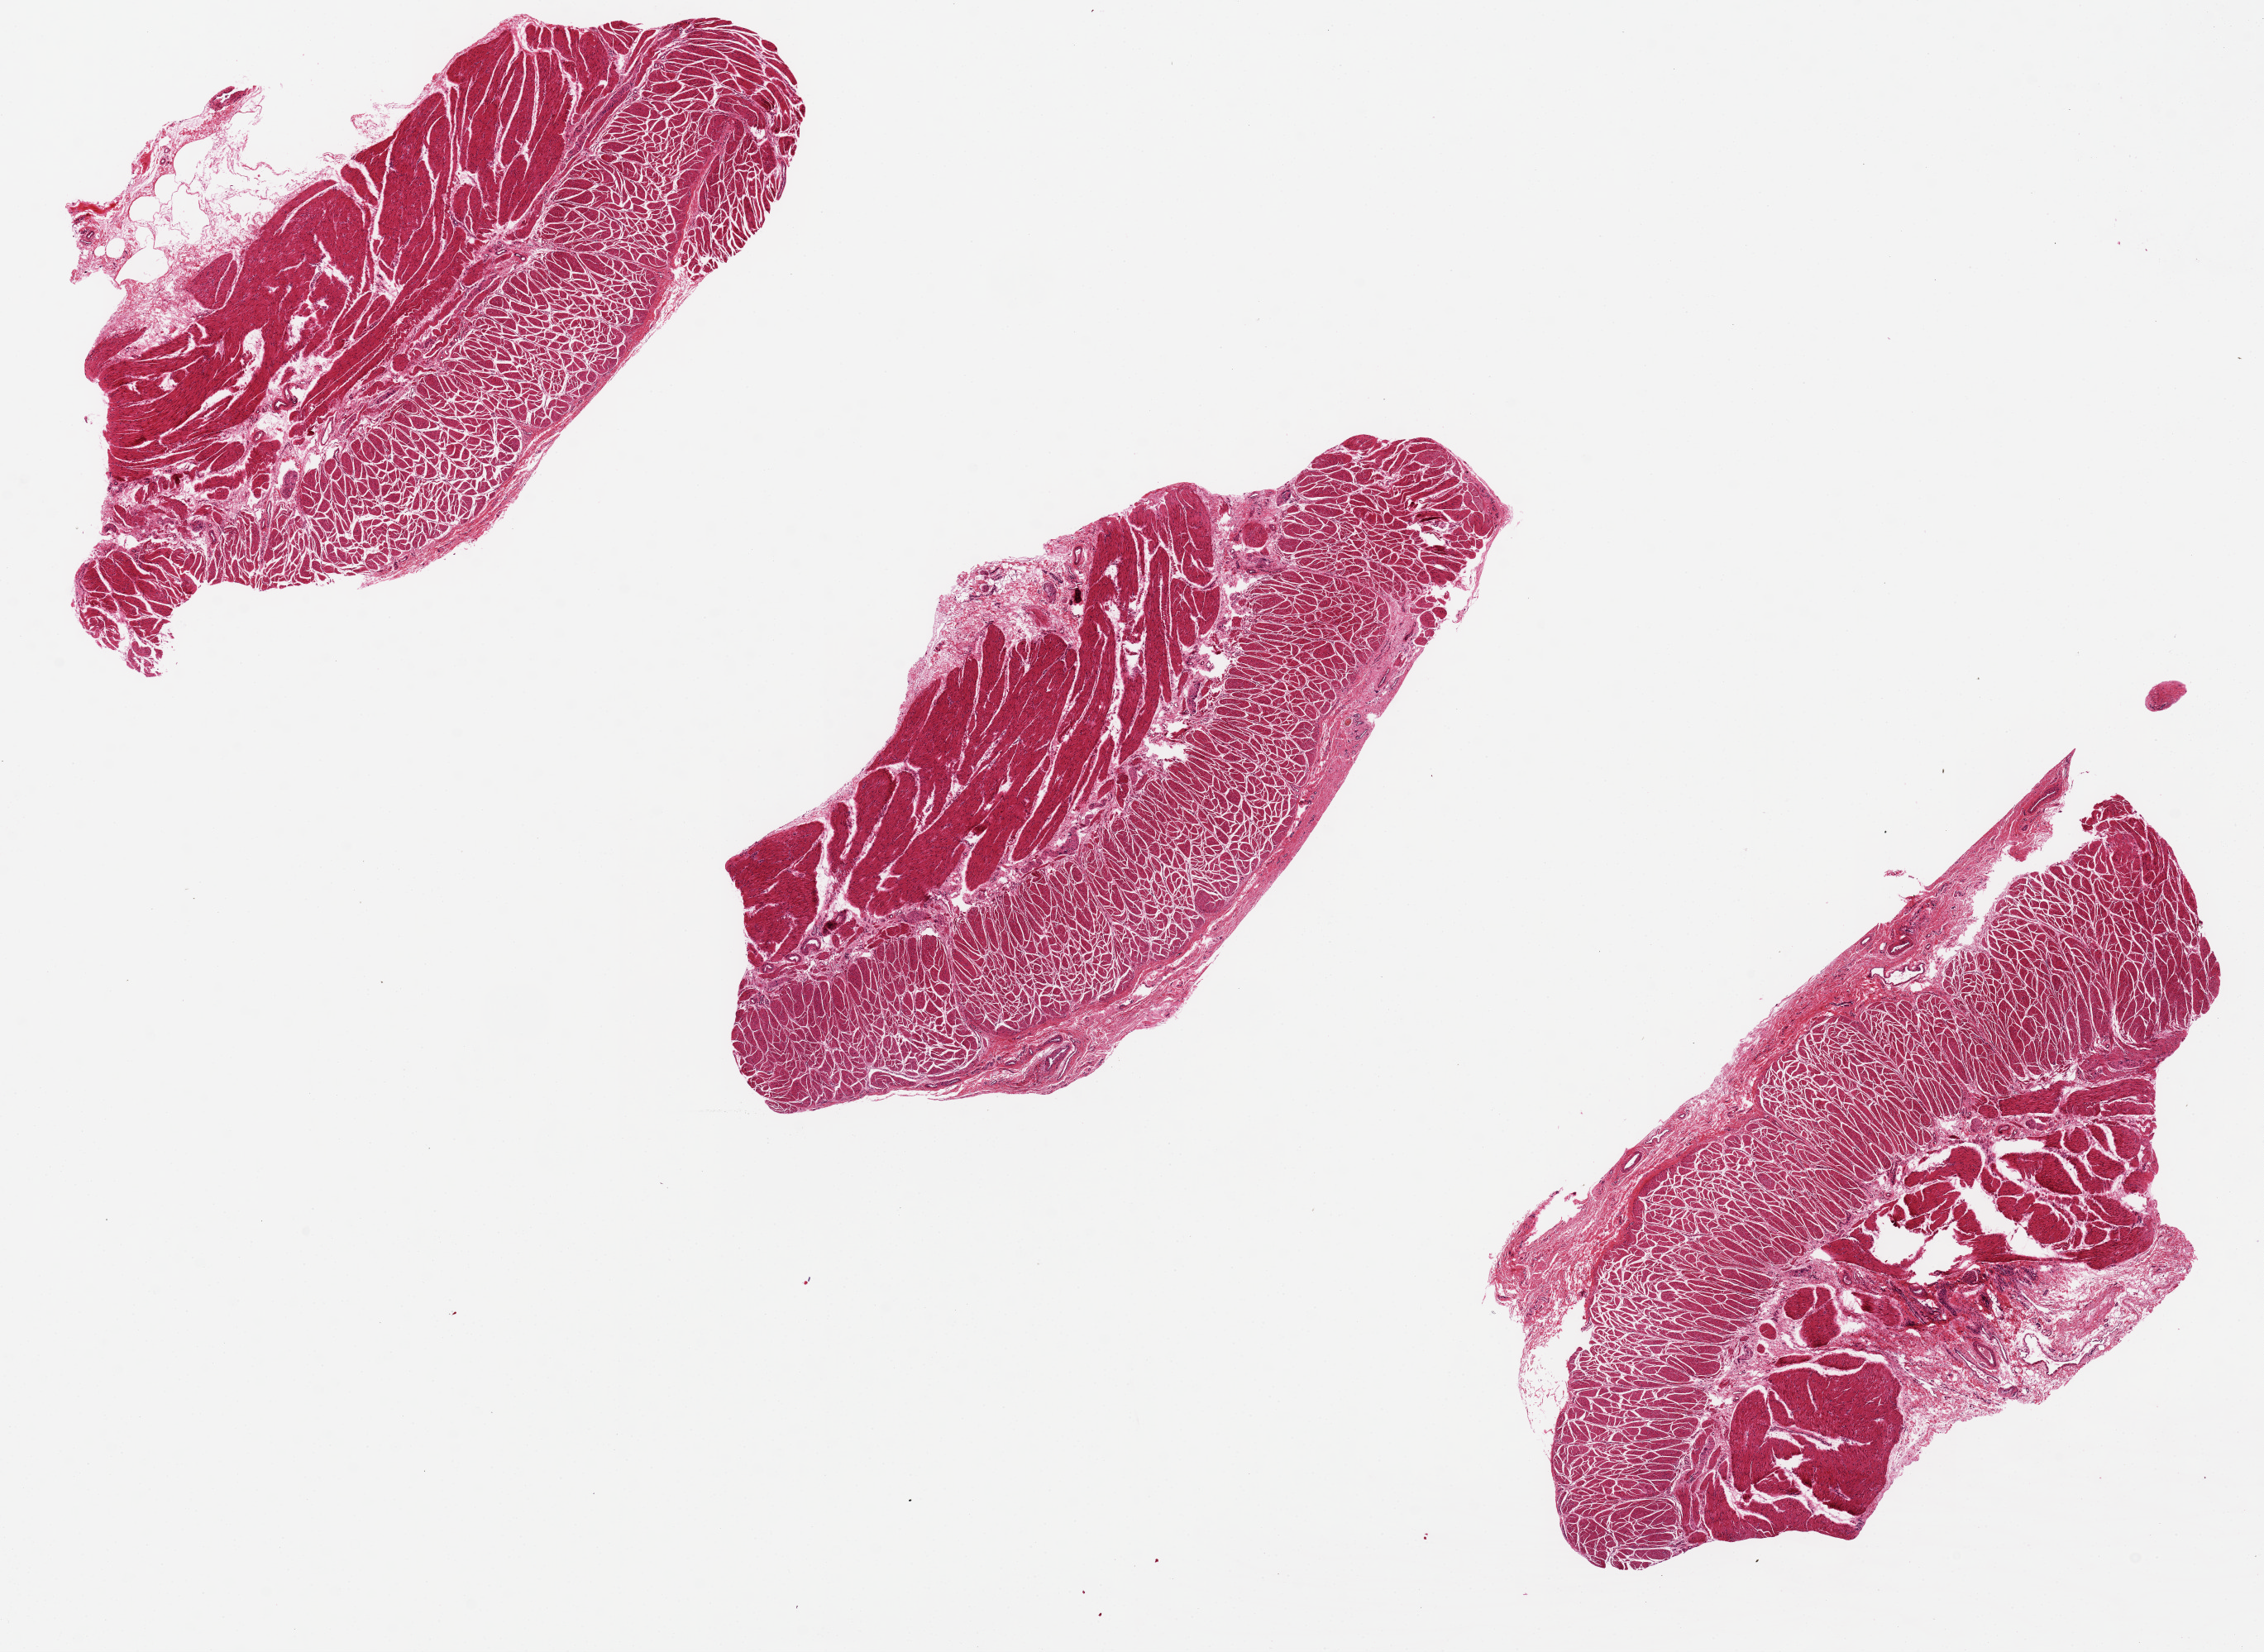
Hematoxylin and eosin (H&E) whole-slide image — a low-resolution overview of the entire scanned area, about 21.7 x 15.8 mm (acquisition: 20x scan). PAXgene-fixed paraffin-embedded (PFPE) section. Sampled site (target tissue): esophageal muscle. Tissue donor sample. Donor sex: female.
Pathologist's review note for this sample: Fracture defects.